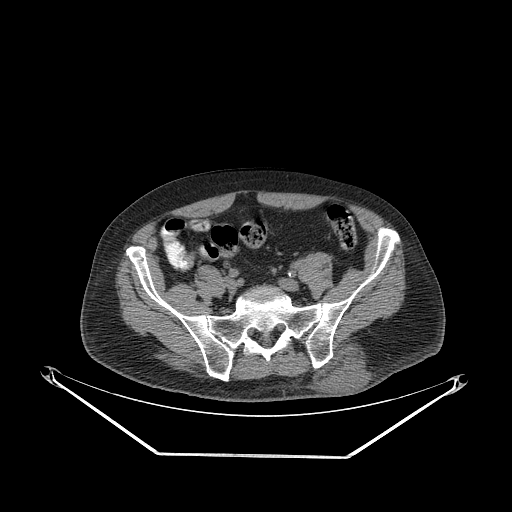
CT of an extremity soft-tissue mass (from a PET/CT study), one axial slice. Position 78 of 267 along the scan axis. Soft-tissue window (W 400 / L 40 HU). 3.75 mm slice thickness. 512 × 512 image matrix, field of view 500 × 500 mm. Male patient. From the clinical record (not read from this slice): histological type: leiomyosarcoma; grade: intermediate; site of the primary tumour: left pelvis.
Annotated regions visible in this slice (expert contour drawn on MRI and transferred to this co-registered scan by the dataset authors):
- gross tumour volume (mass): box from (x=317, y=345) to (x=369, y=396) px